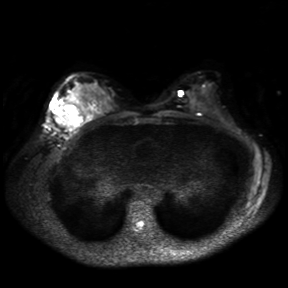
Breast MRI, one axial slice. Position 18 of 30 along the scan axis. Diffusion-weighted series; image 2 of 4 stored at this slice position (different b-values; order by instance number). 3 T. 4 mm slice thickness. 288 × 288 image matrix, field of view 360 × 360 mm. Female patient.
Annotated regions visible in this slice (expert manual segmentation):
- tumour on diffusion-weighted imaging: box from (x=52, y=105) to (x=67, y=127) px